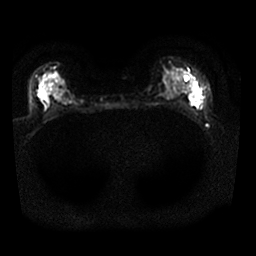
Breast MRI, one axial slice; position 17 of 25 along the scan axis; diffusion-weighted series; image 2 of 4 stored at this slice position (different b-values; order by instance number); 1.5 T; 256 × 256 image matrix, field of view 320 × 320 mm. Female patient.
Annotated regions visible in this slice (manually delineated by an expert):
- tumour on diffusion-weighted imaging: bounding box [x1, y1, x2, y2] px = [188, 89, 200, 105]